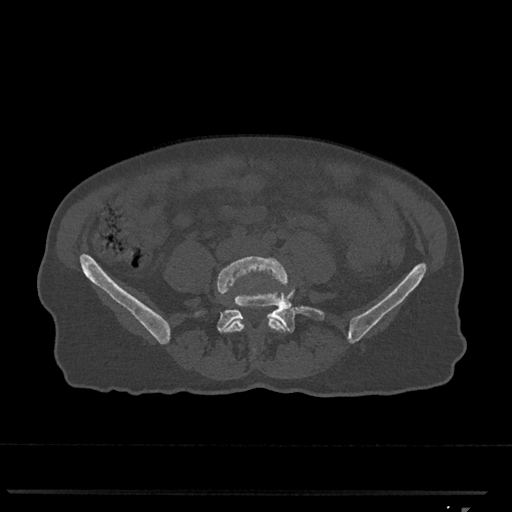
CT including the spine, one axial slice. Position 176 of 793 along the scan axis. Reconstruction kernel Br40s/3. 120 kVp. Bone window (W 1800 / L 400 HU). 0.5 mm slice thickness. 512 × 512 image matrix, field of view 380 × 380 mm. Patient: female, 62 years. From the clinical record (not read from this slice): primary cancer: renal.
Structures marked on this image (semi-automatically segmented with operator editing):
- L4 vertebra: bounding box [x1, y1, x2, y2] px = [217, 256, 289, 352]
- L5 vertebra: [197, 282, 325, 333]